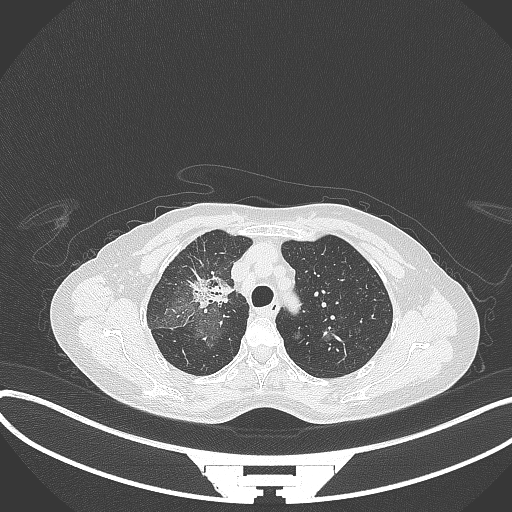
Chest CT, one axial slice; position 243 of 284 along the scan axis; lung window (W 1500 / L -600 HU); 1 mm slice thickness; 512 × 512 image matrix, field of view 400 × 400 mm. Patient: female, 59 years. From the clinical record (not read from this slice): clinical TNM (as recorded): T3 N0 M0.
Structures marked on this image (rectangle marked by the reading radiologist):
- lung tumour (recorded histology: adenocarcinoma): bounding box <188,269,235,308> (left, top, right, bottom; pixels)